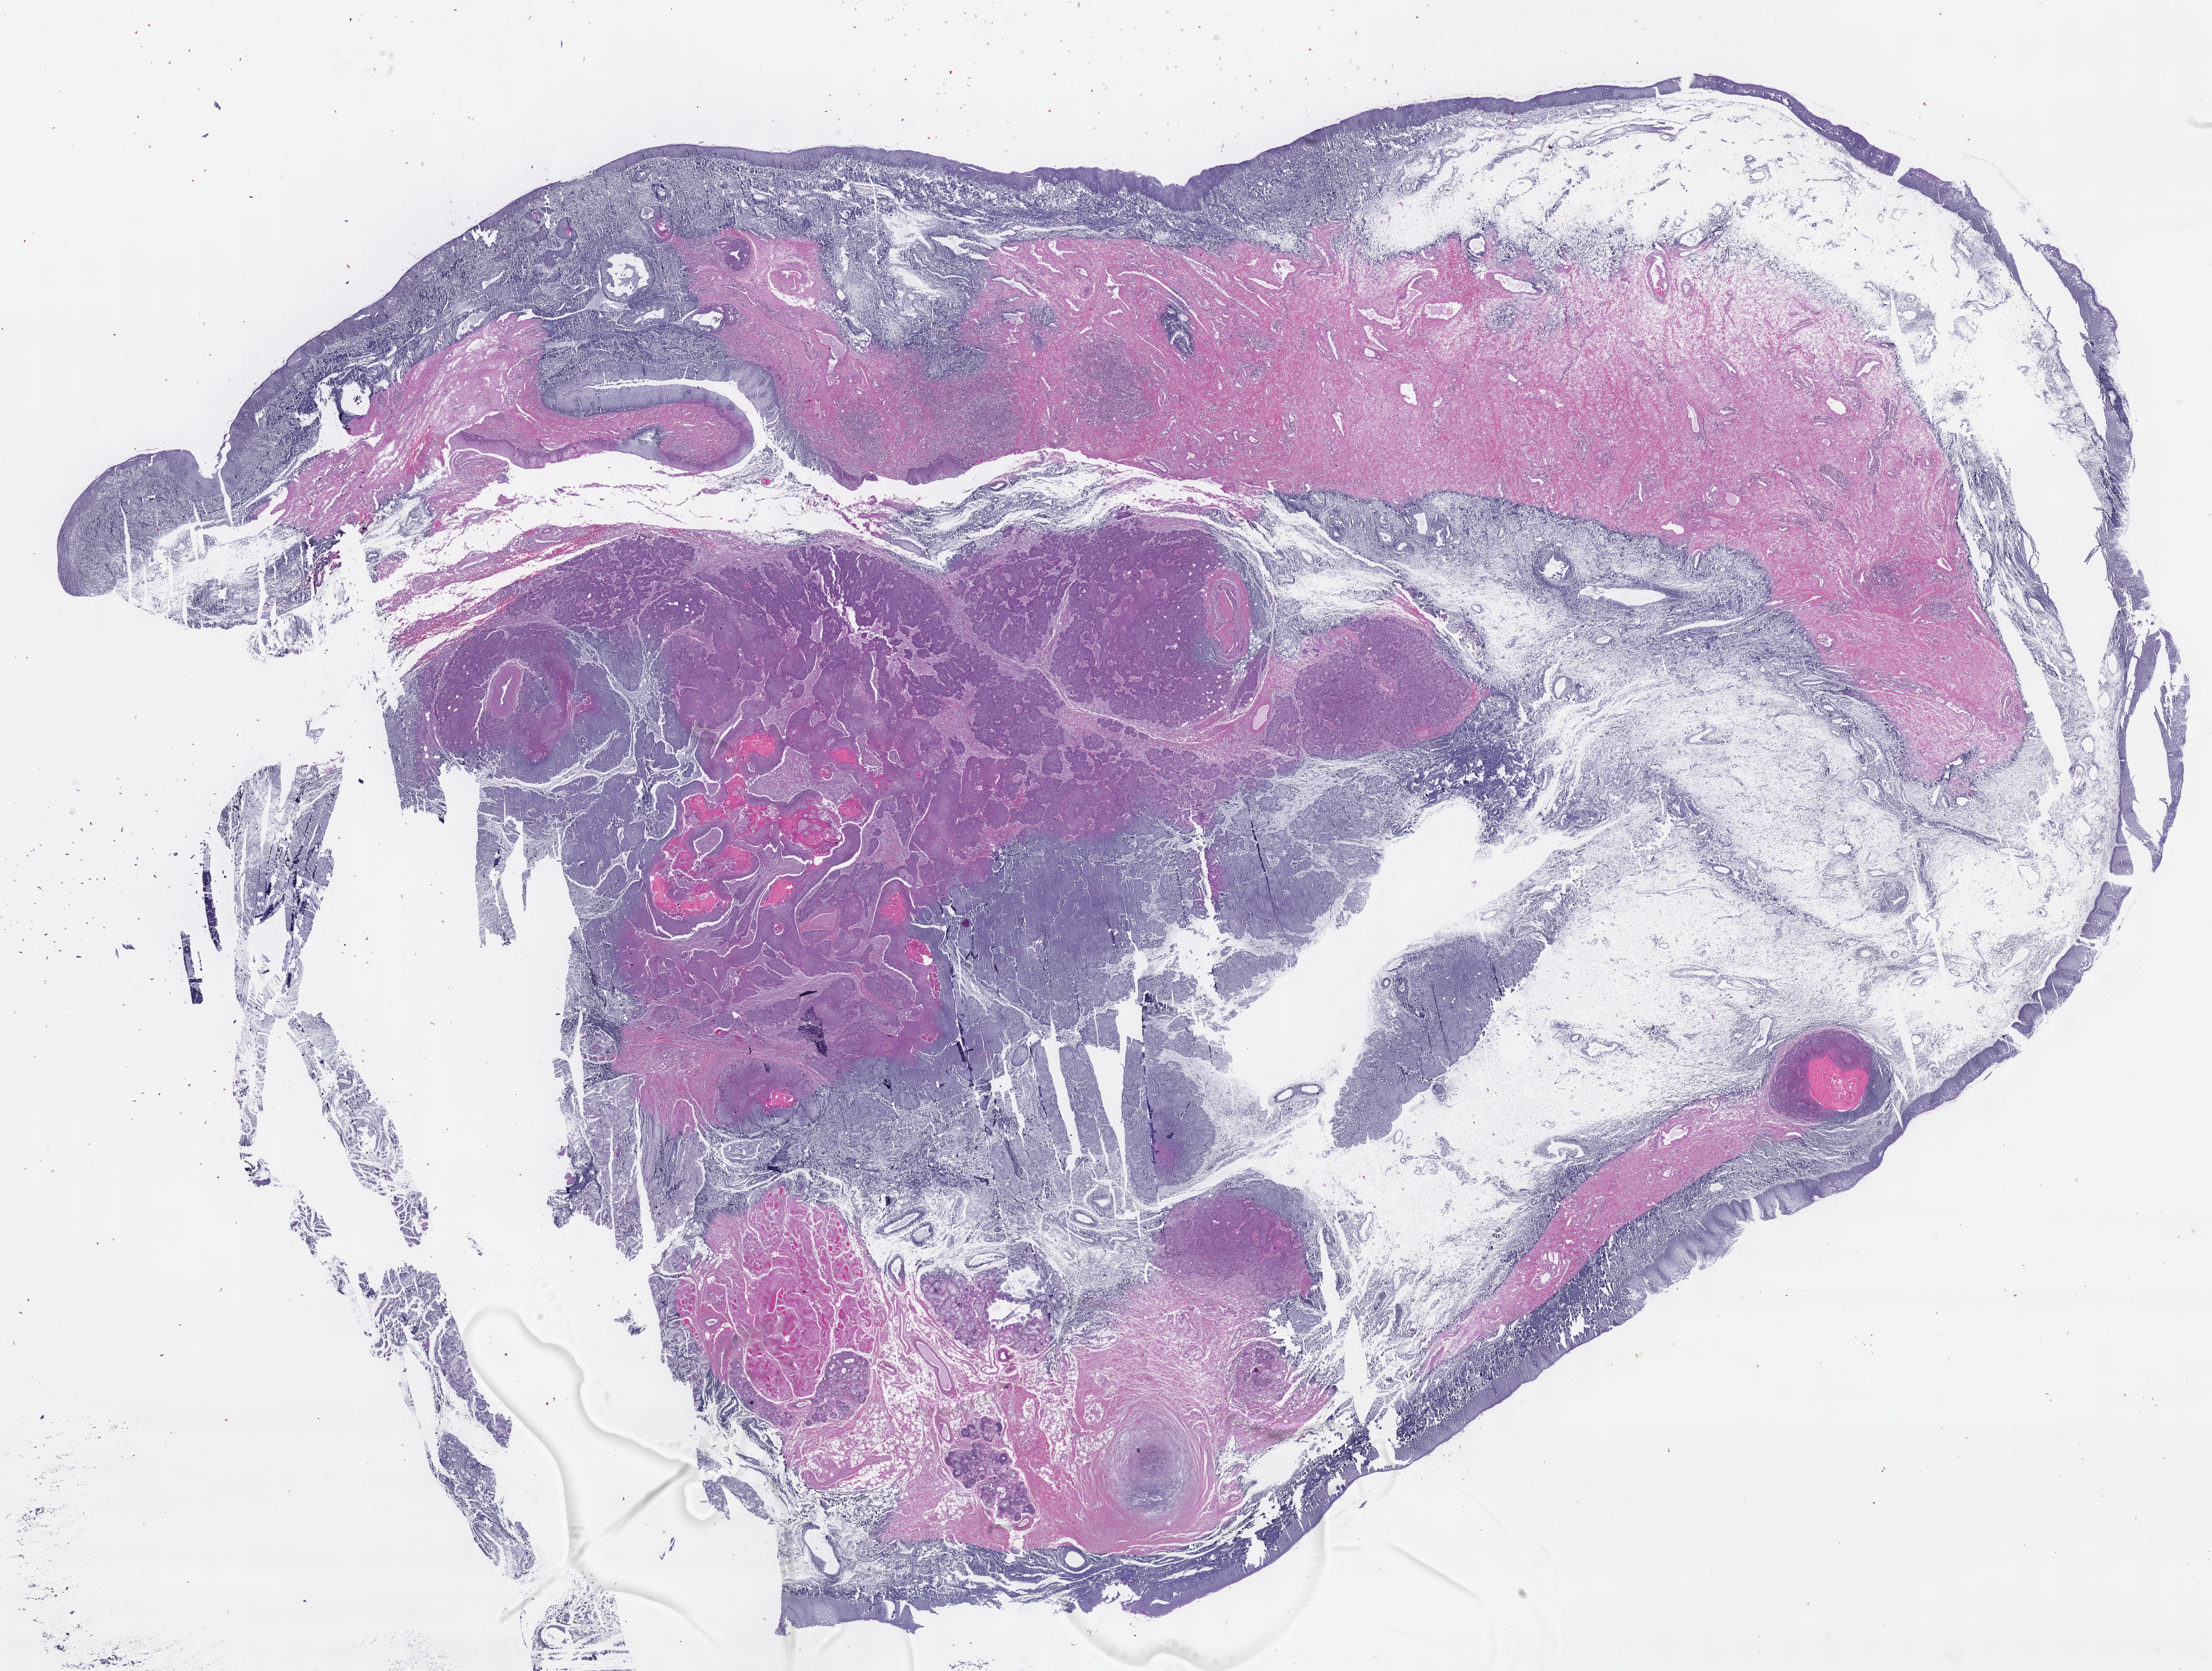
H&E-stained whole-slide image, low-resolution overview of the scanned area, about 27.7 x 20.9 mm. Formalin-fixed paraffin-embedded (FFPE) diagnostic section. Sample: primary tumour, head and neck. Male patient; age at initial diagnosis 66 years. Histologic grade: G2 (moderately differentiated).
Lymph nodes positive (case pathology): 2 of 2 examined. Diagnosis: Squamous cell carcinoma, NOS (tongue, NOS). AJCC pathologic stage: IVA.